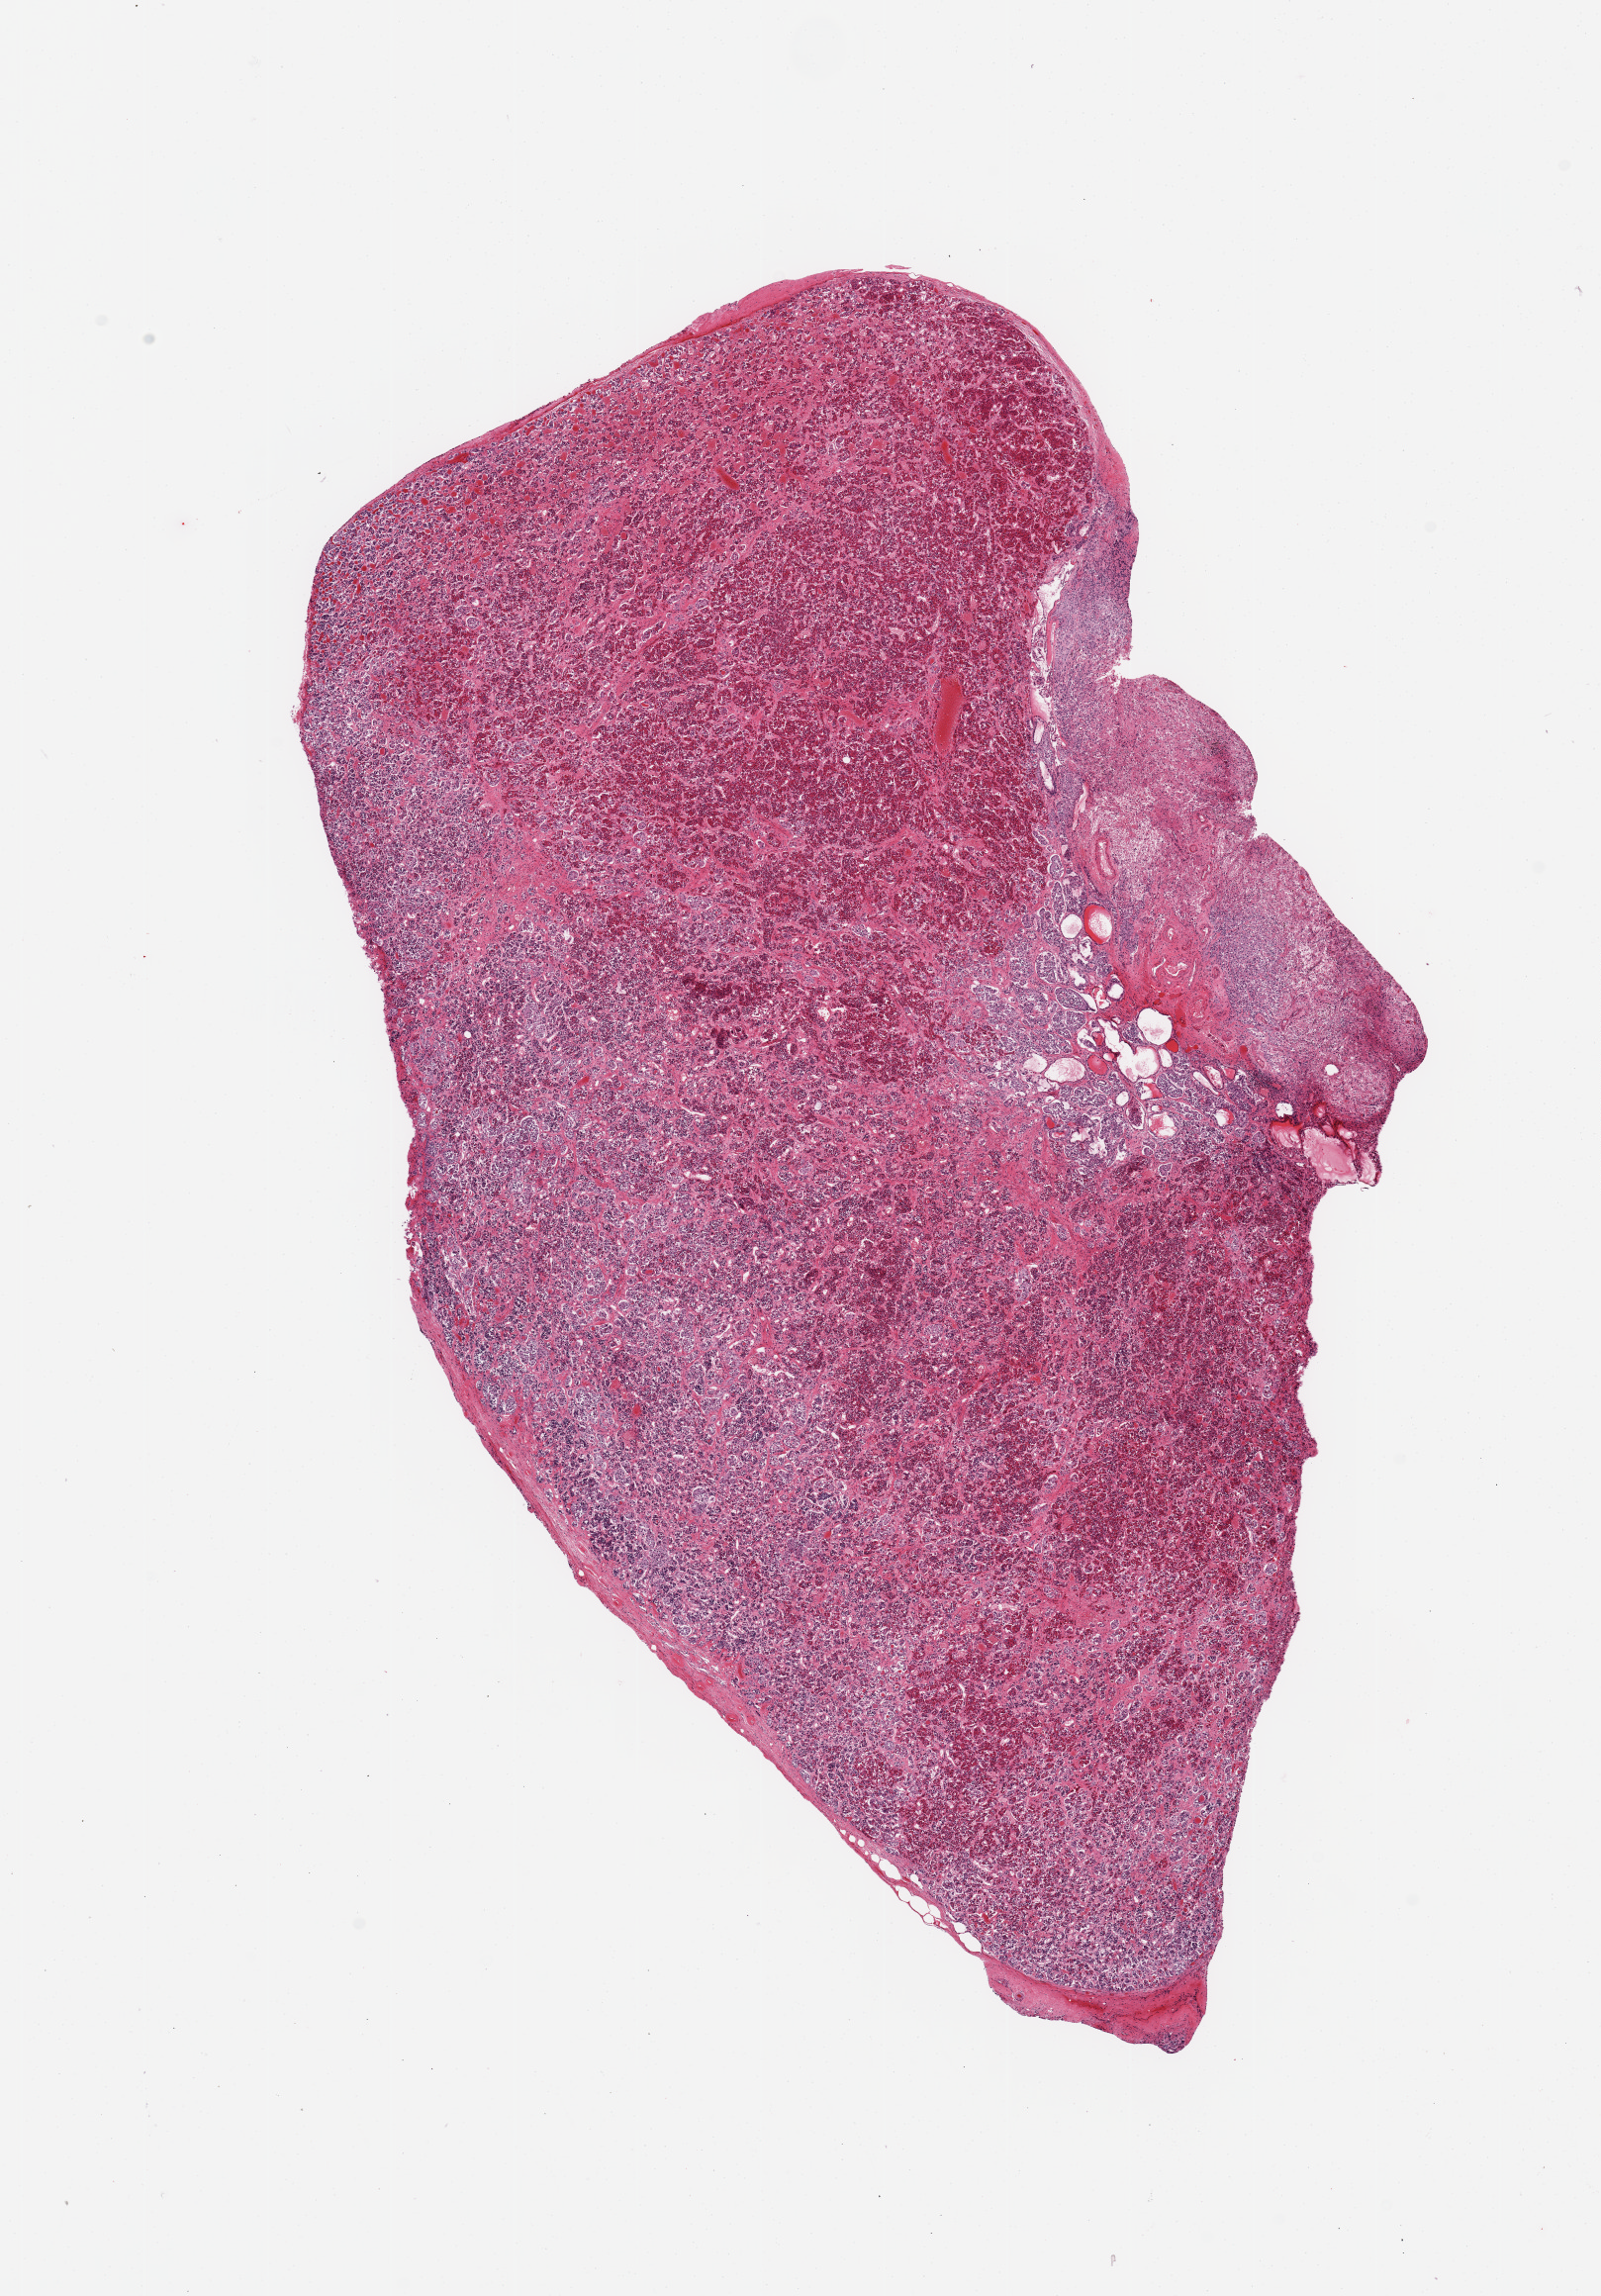
Hematoxylin and eosin (H&E) whole-slide image, a low-resolution overview of the entire scanned area, about 12.8 x 18.3 mm (acquisition: 20x scan); PAXgene-fixed, paraffin-embedded tissue; sampled site (target tissue): pituitary; donor tissue sample. Male donor.
Review note (as recorded): 1 piece; 90% adenohypophysis with mild to moderate autolysis and 10% neurohypophysis; congestion.